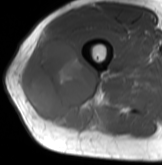
MRI of an extremity soft-tissue mass, one axial slice. Position 44 of 61 along the scan axis. MR volume resampled by the dataset authors to the PET/CT grid (not the native acquisition matrix). 162 × 165 image matrix. Male patient. From the clinical record (not read from this slice): histological type: poorly differentiated synovial sarcoma; grade: high; site of the primary tumour: right buttock.
Structures marked on this image (expert contour drawn on MRI and transferred to this co-registered scan by the dataset authors):
- gross tumour volume including surrounding oedema: bounding box <22,31,108,130> (left, top, right, bottom; pixels)
- gross tumour volume (mass): <22,33,104,130>